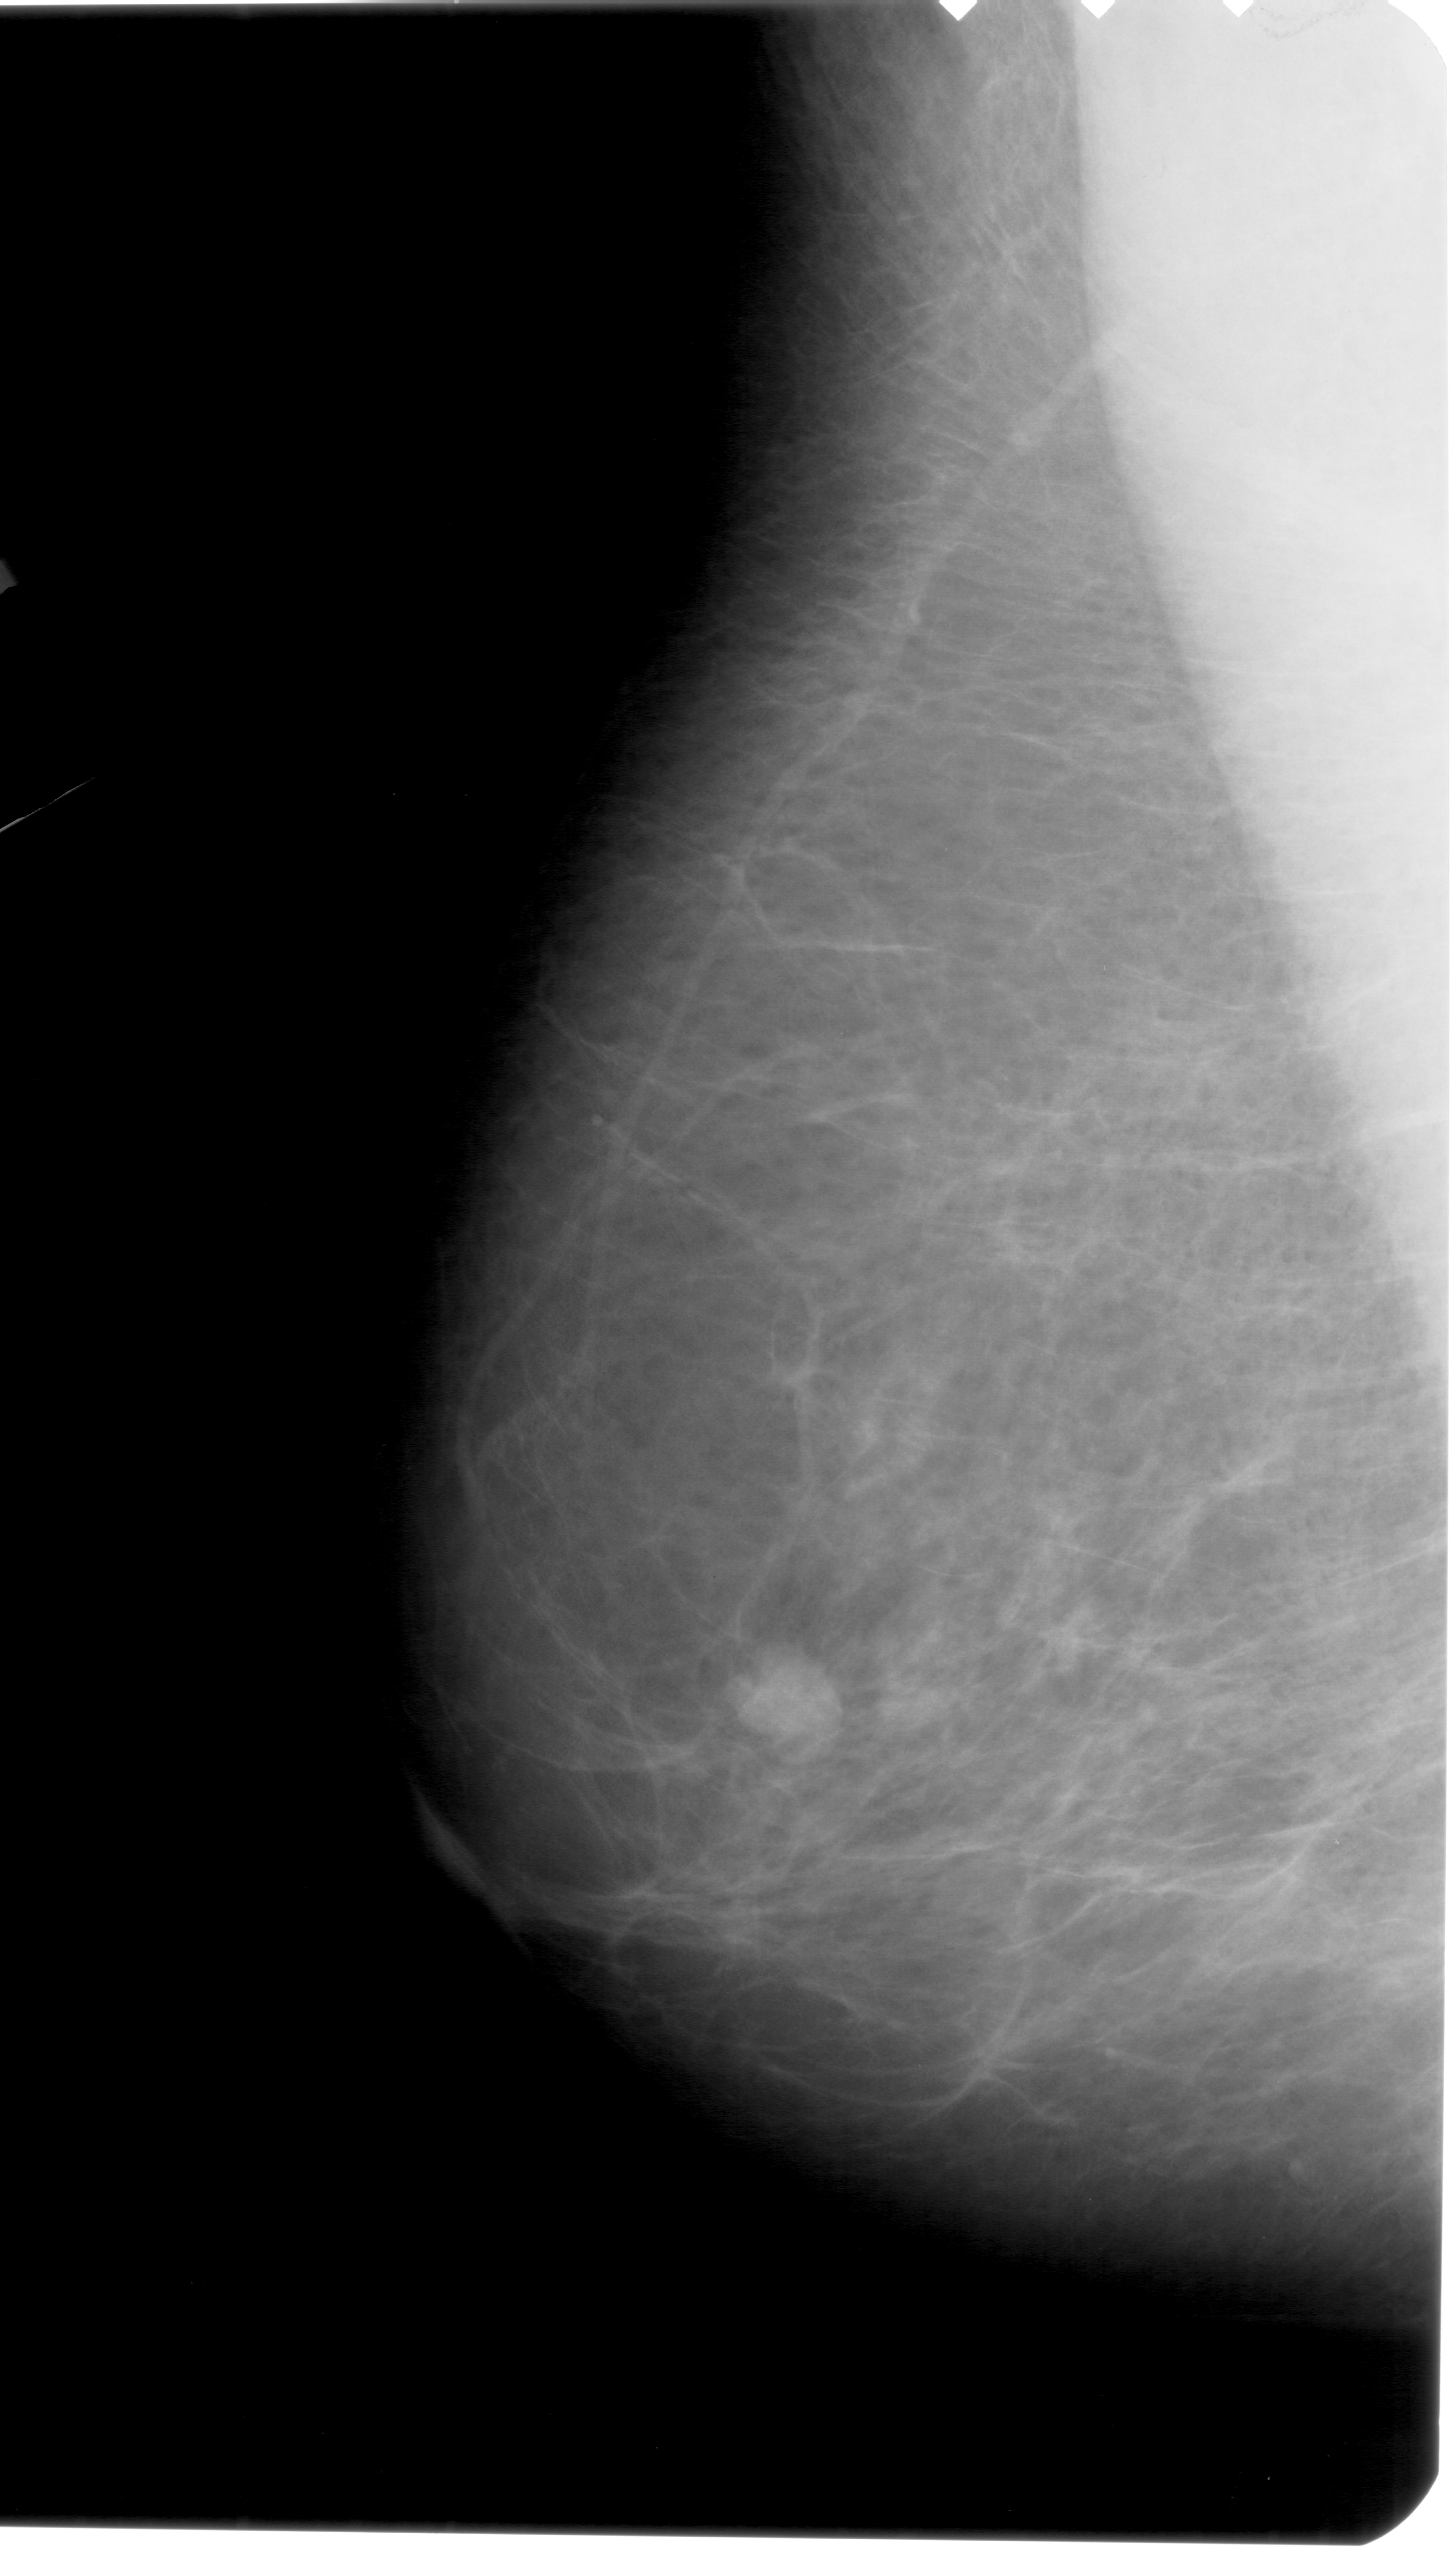
Digitized screen-film mammogram, left breast, mediolateral oblique (MLO) view, BI-RADS breast density category 3 (scale 1–4).
Mass, shape lobulated, margins circumscribed; BI-RADS assessment category 4; subtlety rating 5 on a 1 (subtle) to 5 (obvious) scale; pathology (as recorded): malignant.